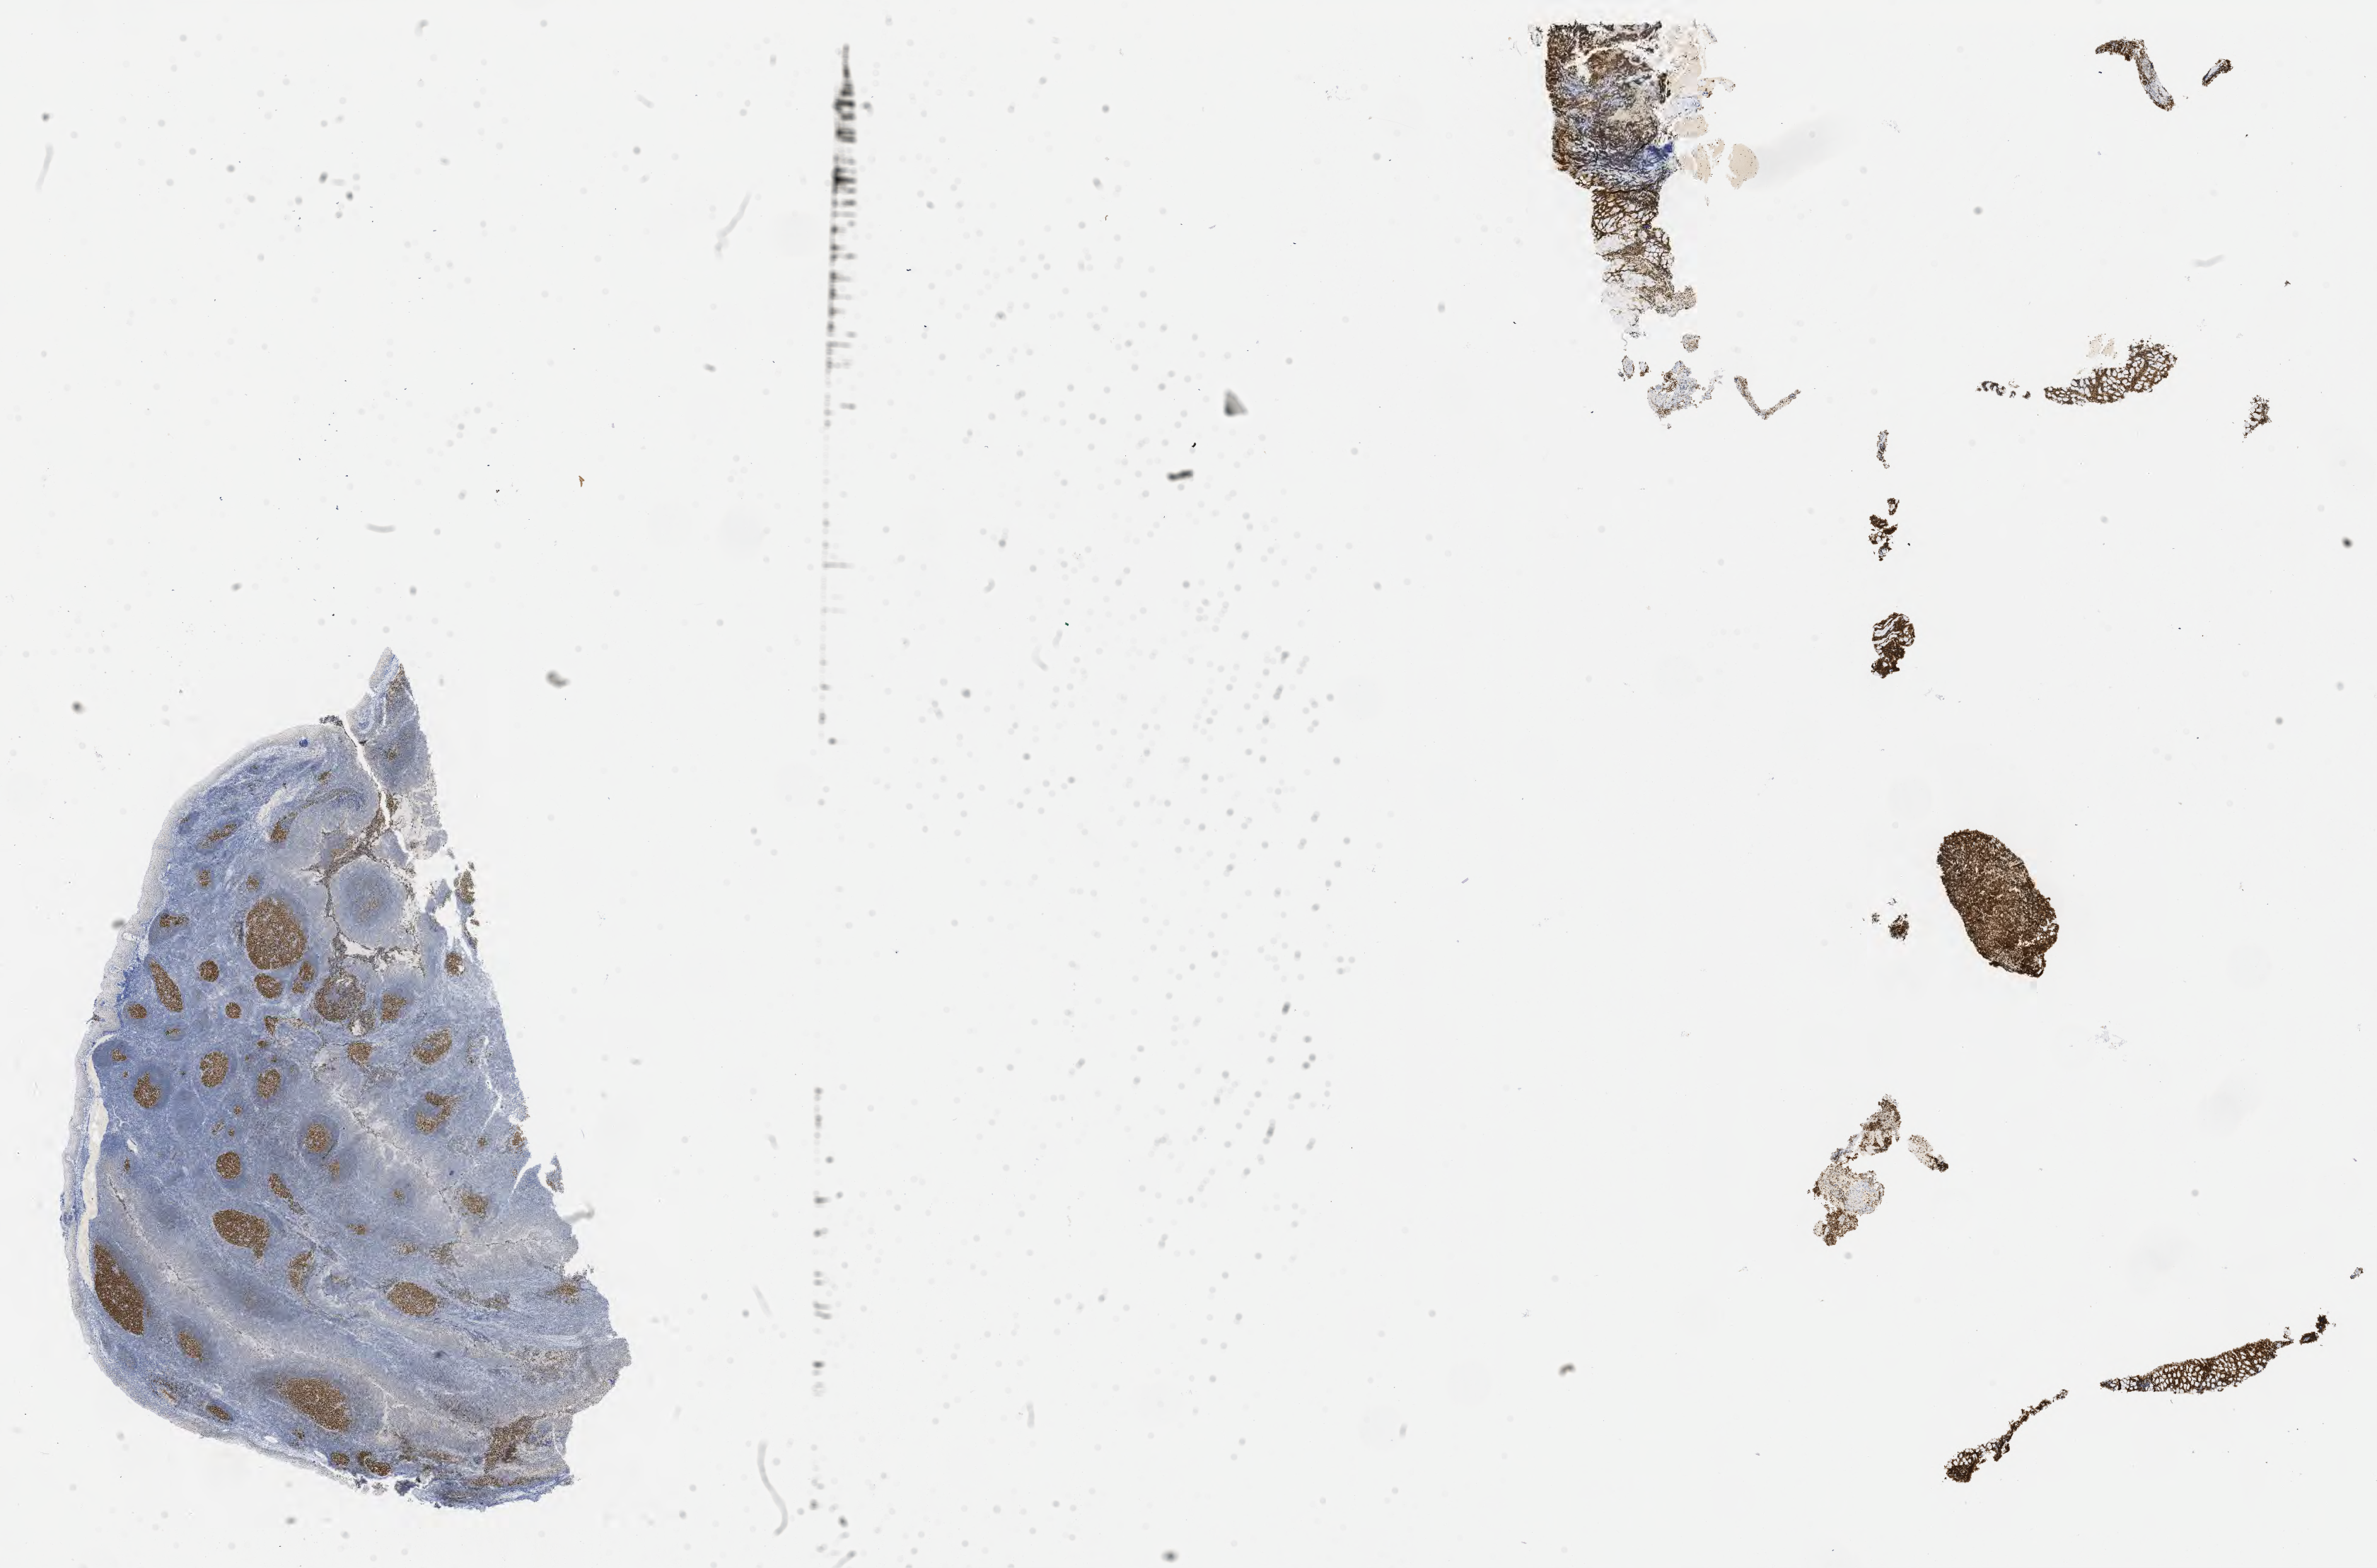
Whole-slide image, immunohistochemical stain for BCL6, whole scanned area (about 27.2 x 17.9 mm) shown as a low-resolution overview; specimen: tumor tissue; site: bone of pelvis. Patient: male, 53 years old.
• diagnosis: Burkitt lymphoma, NOS